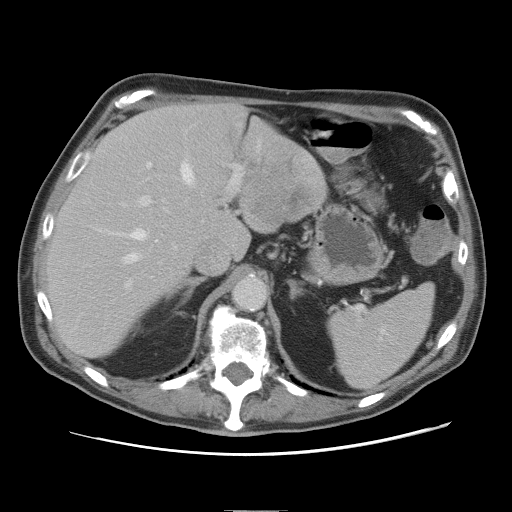
Contrast-enhanced abdominal CT, one axial slice; slice 53 of 89 in the series (ordered by position); soft-tissue window (W 400 / L 40 HU); 5 mm slice thickness; 512 × 512 image matrix, field of view 375 × 375 mm. Male patient, age 69 years. From the clinical record (not read from this slice): diagnosis: colorectal cancer liver metastases, imaged before liver resection; multiple liver metastases: no.
Annotated regions visible in this slice (expert manual segmentation):
- hepatic veins: bounding box [x1, y1, x2, y2] px = [125, 162, 196, 264]
- liver: [48, 104, 327, 358]
- planned liver remnant (the part of the liver to remain after resection): [49, 104, 247, 358]
- portal vein (with intrahepatic branches): [127, 141, 261, 286]
- liver metastasis: [249, 183, 310, 224]